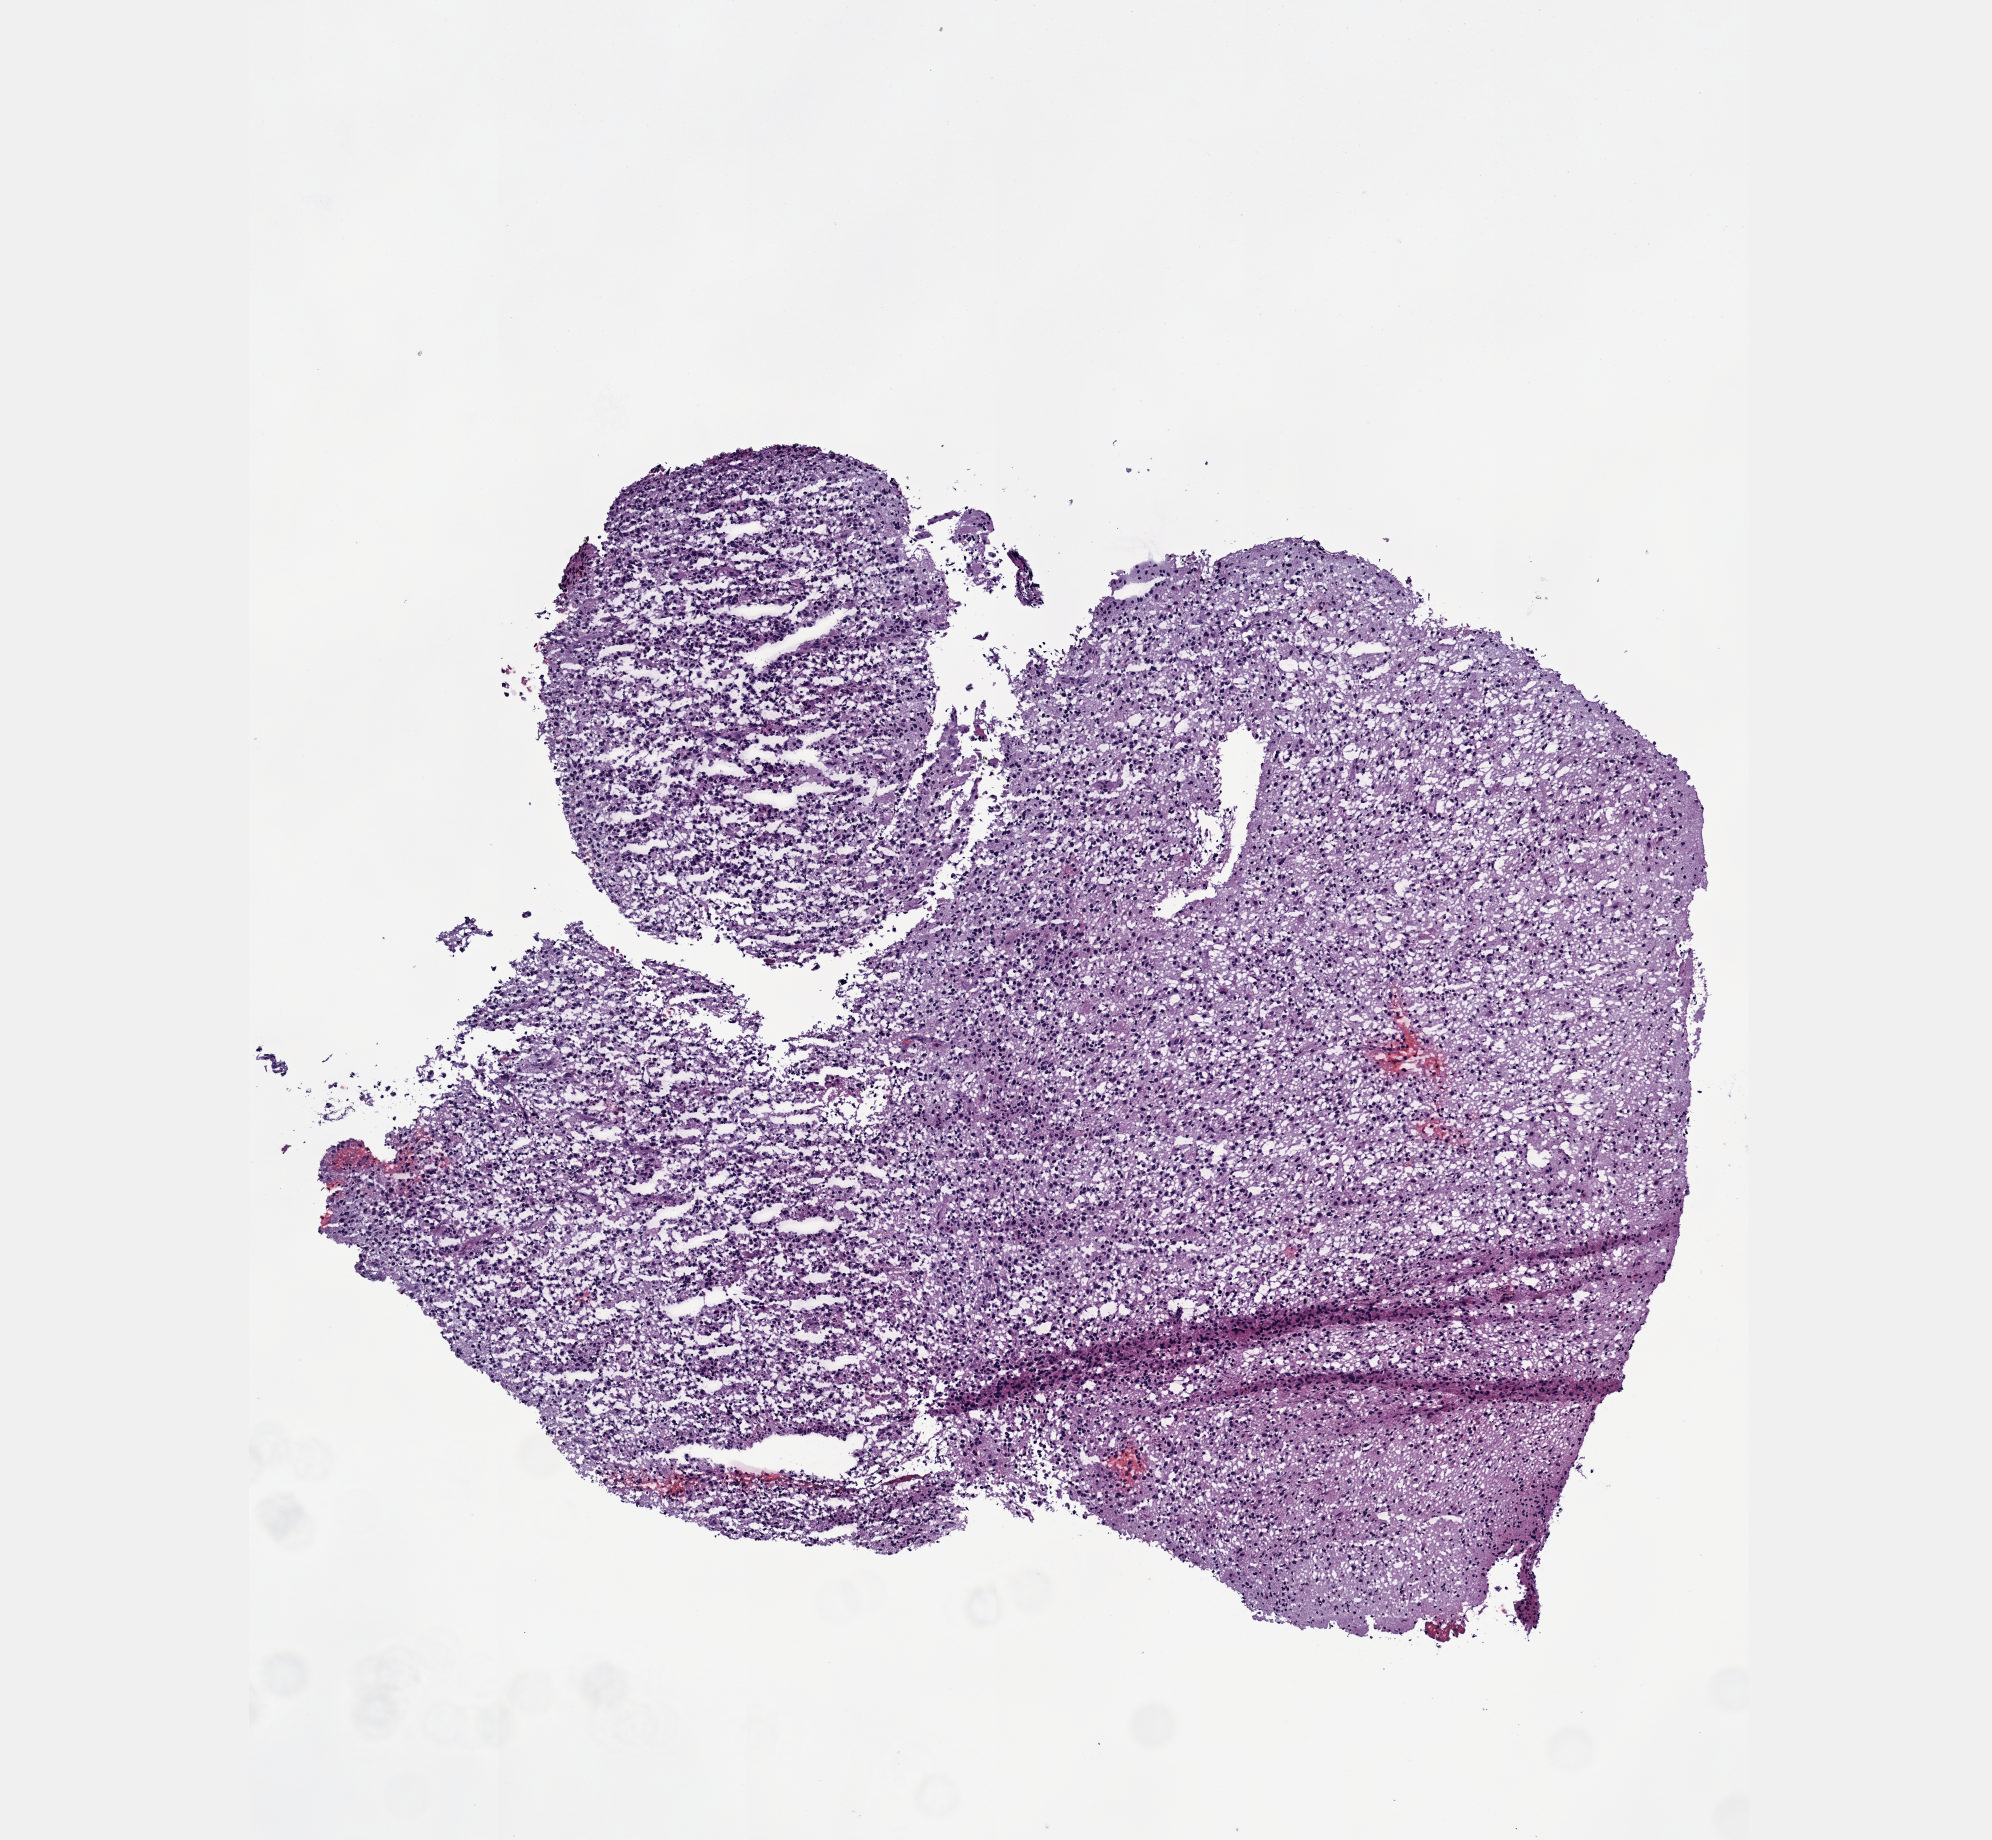
Whole-slide histology image, H&E, whole scanned area (about 4.0 x 3.7 mm) shown as a low-resolution overview; frozen section from the top of the tissue portion; brain, primary tumour sample. Female, age 45 years at initial diagnosis. Histologic grade: G3 (poorly differentiated). Composition of this section per pathologist review: tumour cells 50%, tumour nuclei 90%, normal cells 10%, stromal cells 40%, necrosis 0%. Inflammatory infiltration, as recorded: lymphocyte infiltration 0%, monocyte infiltration 0%, neutrophil infiltration 0%.
- histologic diagnosis: Astrocytoma, anaplastic (cerebrum)